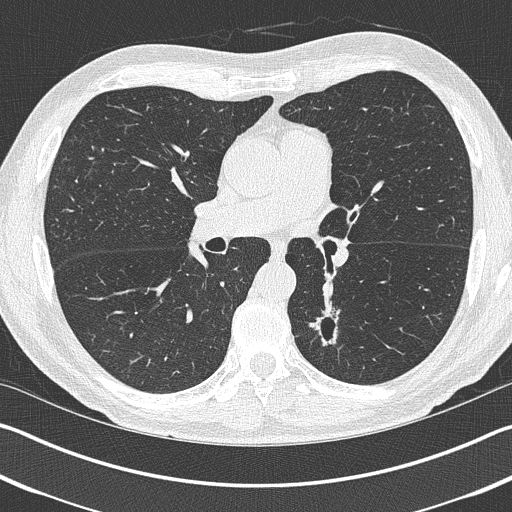
Chest CT (low-dose screening protocol), one axial image. First (baseline) screen. Lung window (W 1500 / L -600 HU). Lung (sharp) reconstruction kernel (B50f). Slice 172 of 402 in the series. Male participant, aged 69 years at enrolment. Current smoker at enrolment.
Expert-annotated lung lesion, bounding box (x1, y1, x2, y2) in pixels: (295, 305, 351, 362). The exam's reader record, not a measurement of the box and not confirmed to be the same lesion: non-calcified nodule or mass ≥4 mm, left upper lobe, 19 × 19 mm, spiculated (stellate) margins, pre-existing on the prior screen: yes. Official screen result: positive, change unspecified: nodule(s) >= 4 mm or enlarging nodule(s), mass(es), or other non-specific abnormalities suspicious for lung cancer. Lung cancer was diagnosed 202 days after this screen: non-small cell carcinoma, left lower lobe, stage IIIA (AJCC 6th edition), 20 mm at pathology.